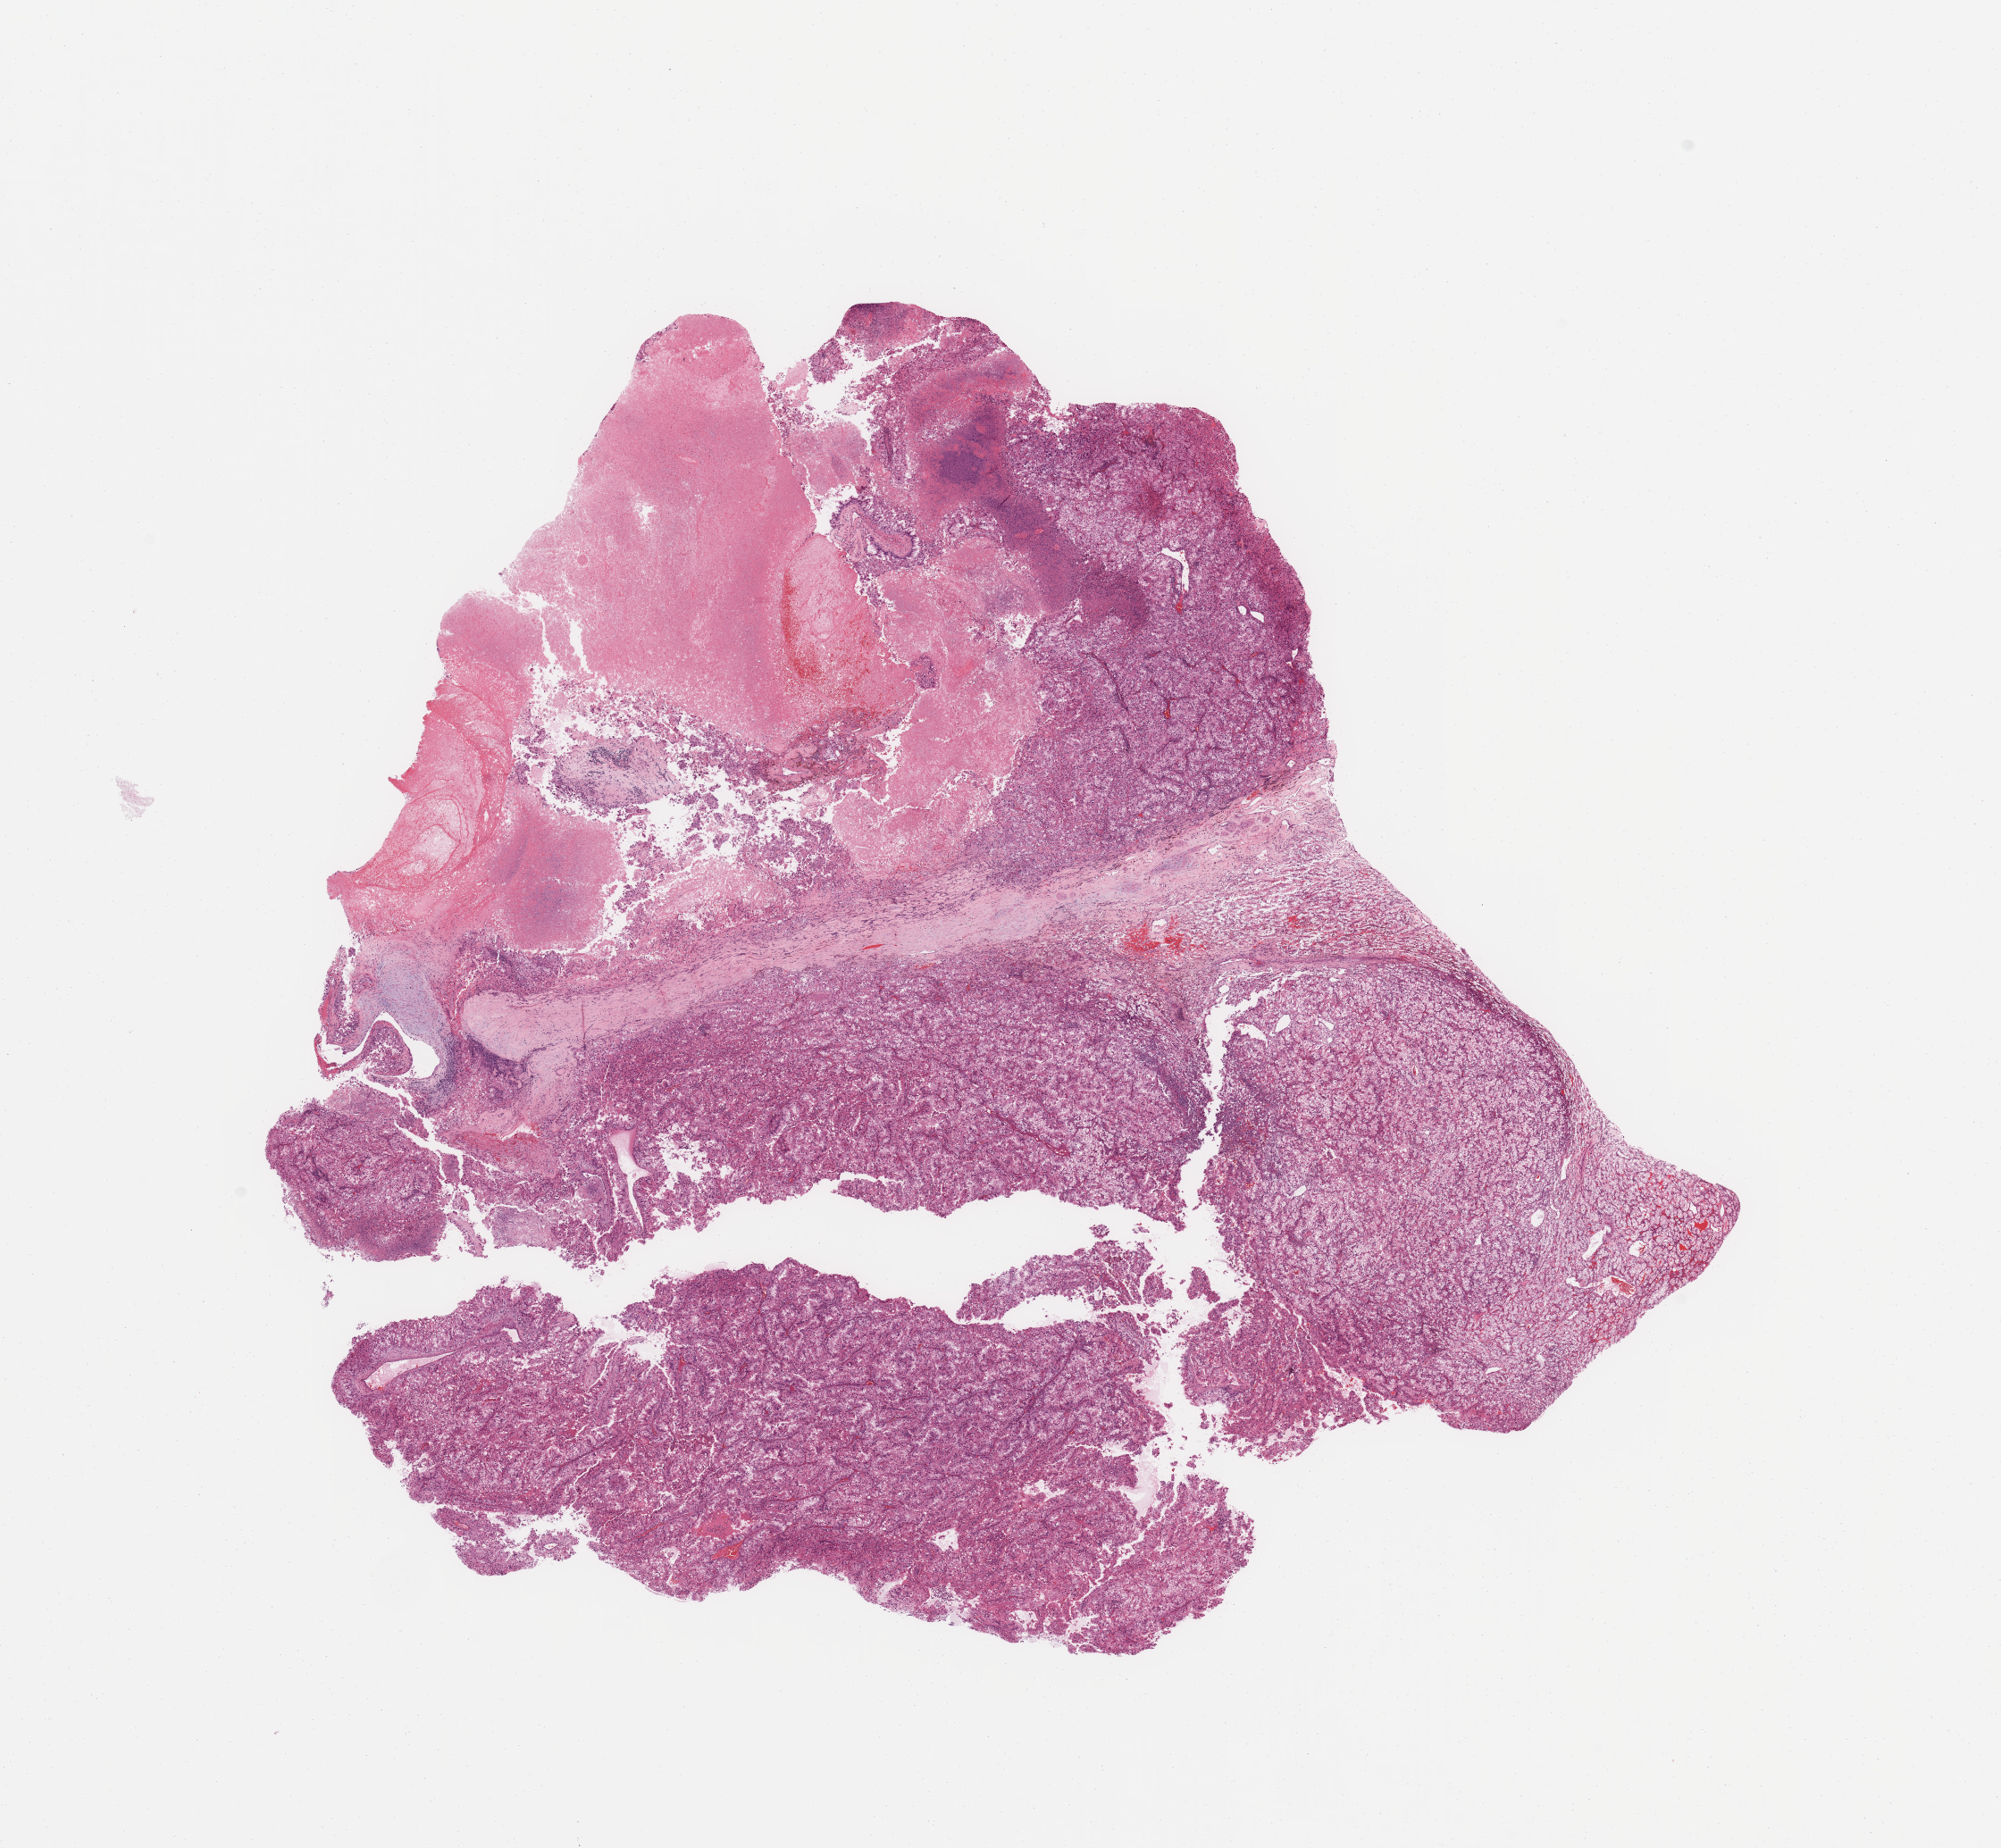
H&E-stained whole-slide image — shown as a low-resolution overview of the whole scanned area (about 17.7 x 16.4 mm), kidney, tumour tissue. Male, 50 y/o. Histologic grade: G4 (undifferentiated).
AJCC pathologic stage: III. Primary tumour site (as recorded): middle. Diagnosis: Renal cell carcinoma, NOS.